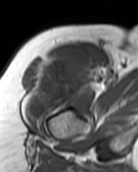
MRI of an extremity soft-tissue mass, one axial slice; position 79 of 99 along the scan axis; MR volume resampled by the dataset authors to the PET/CT grid (not the native acquisition matrix); 3.27 mm slice thickness; 138 × 172 image matrix, field of view 135 × 168 mm. Female patient. Case-level facts recorded for this patient, not image findings: histological type: pleiomorphic undifferentiated sarcoma; grade: high; site of the primary tumour: right quadricep.
Outlined on this slice (expert contour drawn on MRI and transferred to this co-registered scan by the dataset authors):
- gross tumour volume including surrounding oedema: box from (x=26, y=52) to (x=93, y=119) px
- gross tumour volume (mass): (x=28, y=52)–(x=93, y=117)